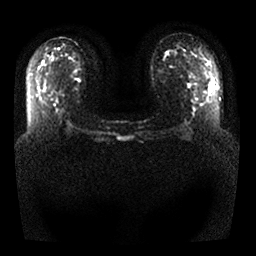
Breast MRI, one axial slice; slice 16 of 25 in the series (ordered by position); diffusion-weighted series; image 2 of 4 stored at this slice position (different b-values; order by instance number); 1.5 T; 4 mm slice thickness; 256 × 256 image matrix, field of view 340 × 340 mm. Female patient.
Annotated regions visible in this slice (outlined manually by an expert reader):
- tumour on diffusion-weighted imaging: bounding box (x1, y1, x2, y2) in pixels: (209, 84, 212, 91)